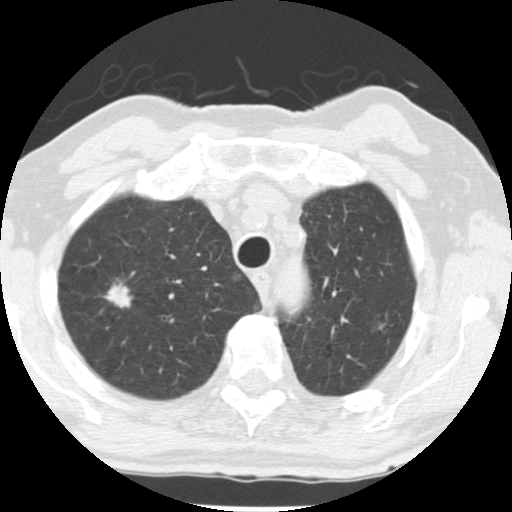
Low-dose screening chest CT, one axial slice. Position 205 of 252 along the scan axis. Reconstruction kernel STANDARD. Lung window (W 1500 / L -600 HU). 2.5 mm slice thickness. 512 × 512 image matrix, field of view 313 × 313 mm.
Outlined on this slice (expert manual segmentation):
- lesion 1 (tumor, upper lobe of right lung): bounding box (x1, y1, x2, y2) in pixels: (104, 281, 133, 308)